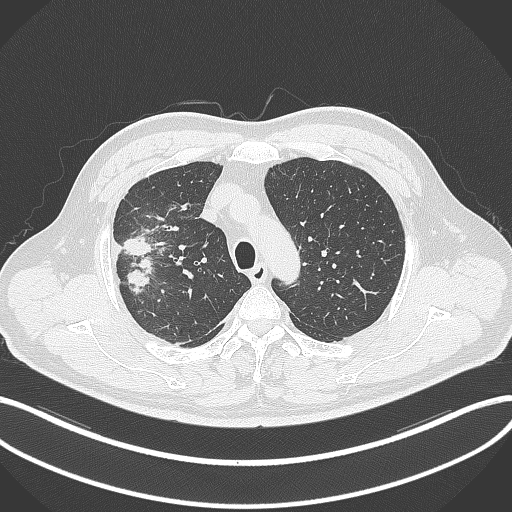
Chest CT, one axial slice; slice 263 of 348 in the series (ordered by position); reconstruction kernel B70f; lung window (W 1500 / L -600 HU); 512 × 512 image matrix, field of view 400 × 400 mm. Male patient, age 55 years. Case-level facts recorded for this patient, not image findings: clinical TNM (as recorded): T3 N2 M1.
Structures marked on this image (bounding box drawn by a radiologist):
- lung tumour (recorded histology: adenocarcinoma): bounding box [x1, y1, x2, y2] px = [119, 234, 159, 296]